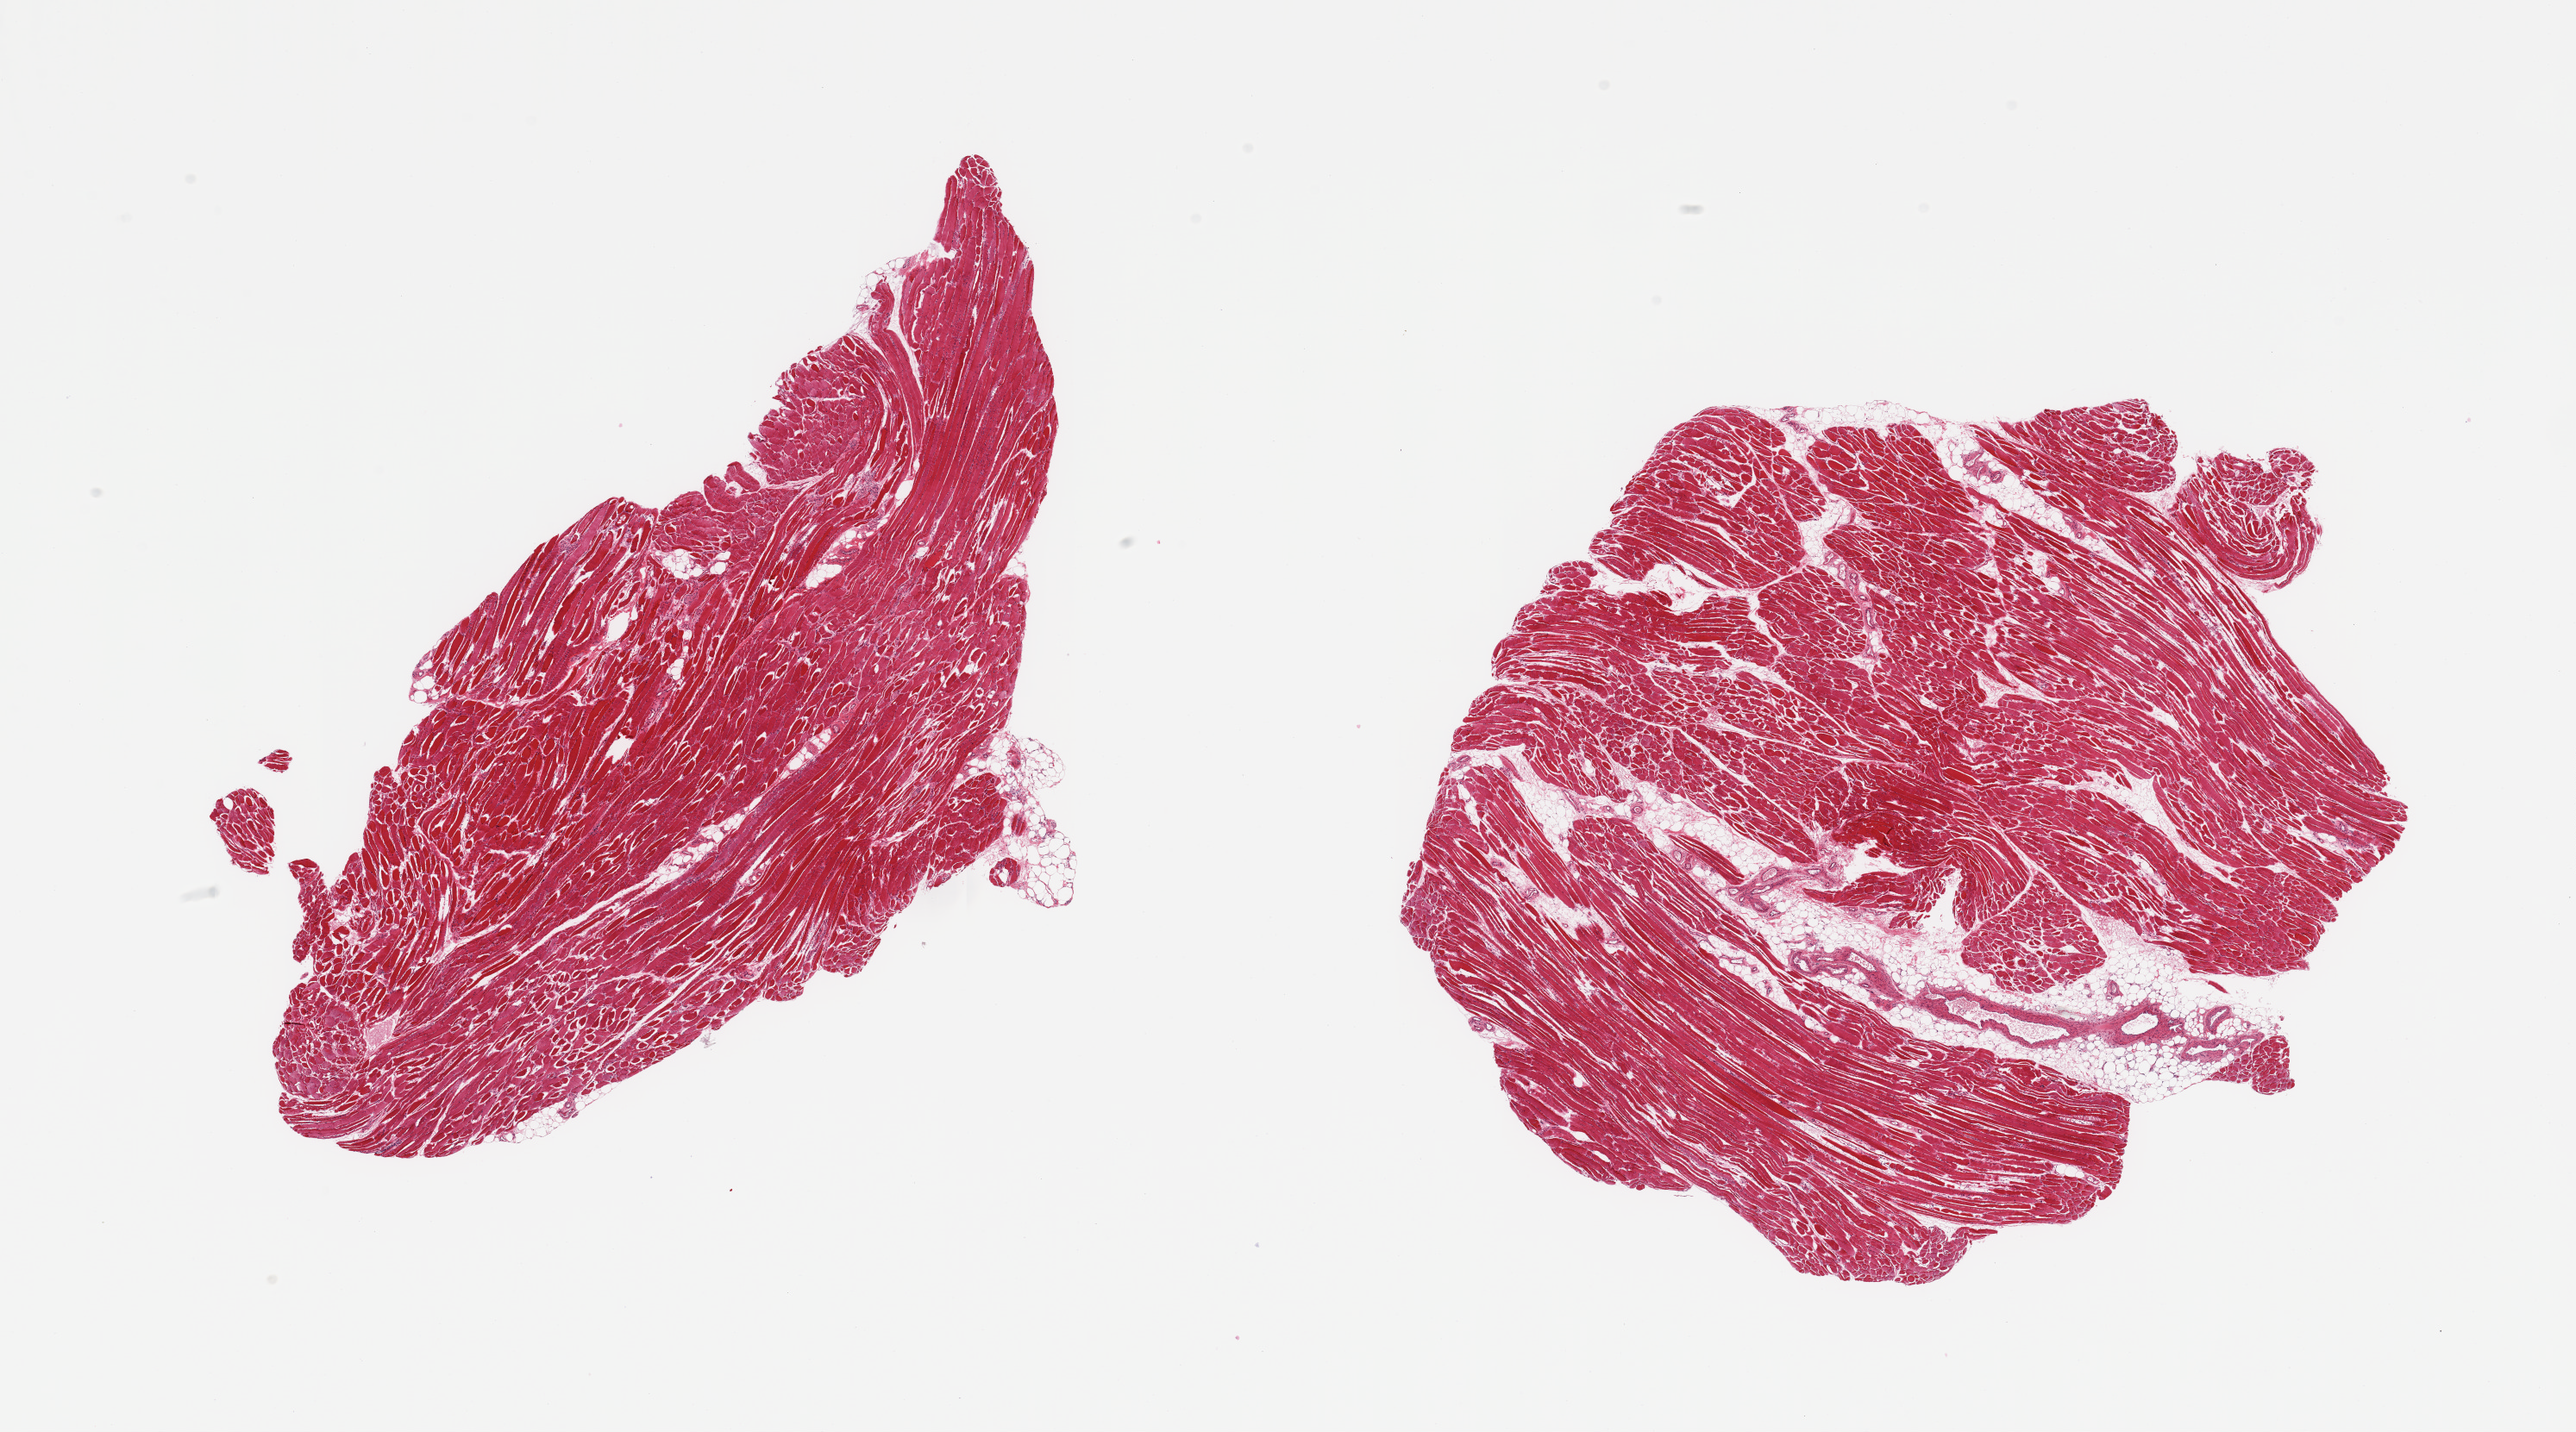
Whole-slide image, H&E stain — a low-resolution overview of the entire scanned area, about 23.6 x 13.1 mm (acquisition: 20x scan). PAXgene-fixed paraffin-embedded (PFPE) section. Sampled site (target tissue): skeletal muscle. Tissue donor sample.
- review note (as recorded): 2 pieces; 1 piece includes ~10% fat (mostly internal), few atrophic fibers